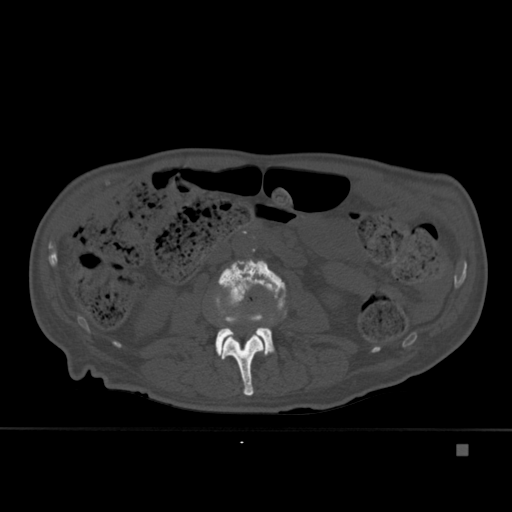
CT including the spine, one axial slice. Position 152 of 451 along the scan axis. Bone window (W 1800 / L 400 HU). 512 × 512 image matrix, field of view 378 × 378 mm. Patient: male, 75 years. Case-level facts recorded for this patient, not image findings: primary cancer: prostate.
Annotated regions visible in this slice (semi-automatic segmentation, software-assisted and operator-edited):
- L2 vertebra: bounding box (x1, y1, x2, y2) in pixels: (221, 313, 265, 396)
- L3 vertebra: (215, 259, 287, 359)